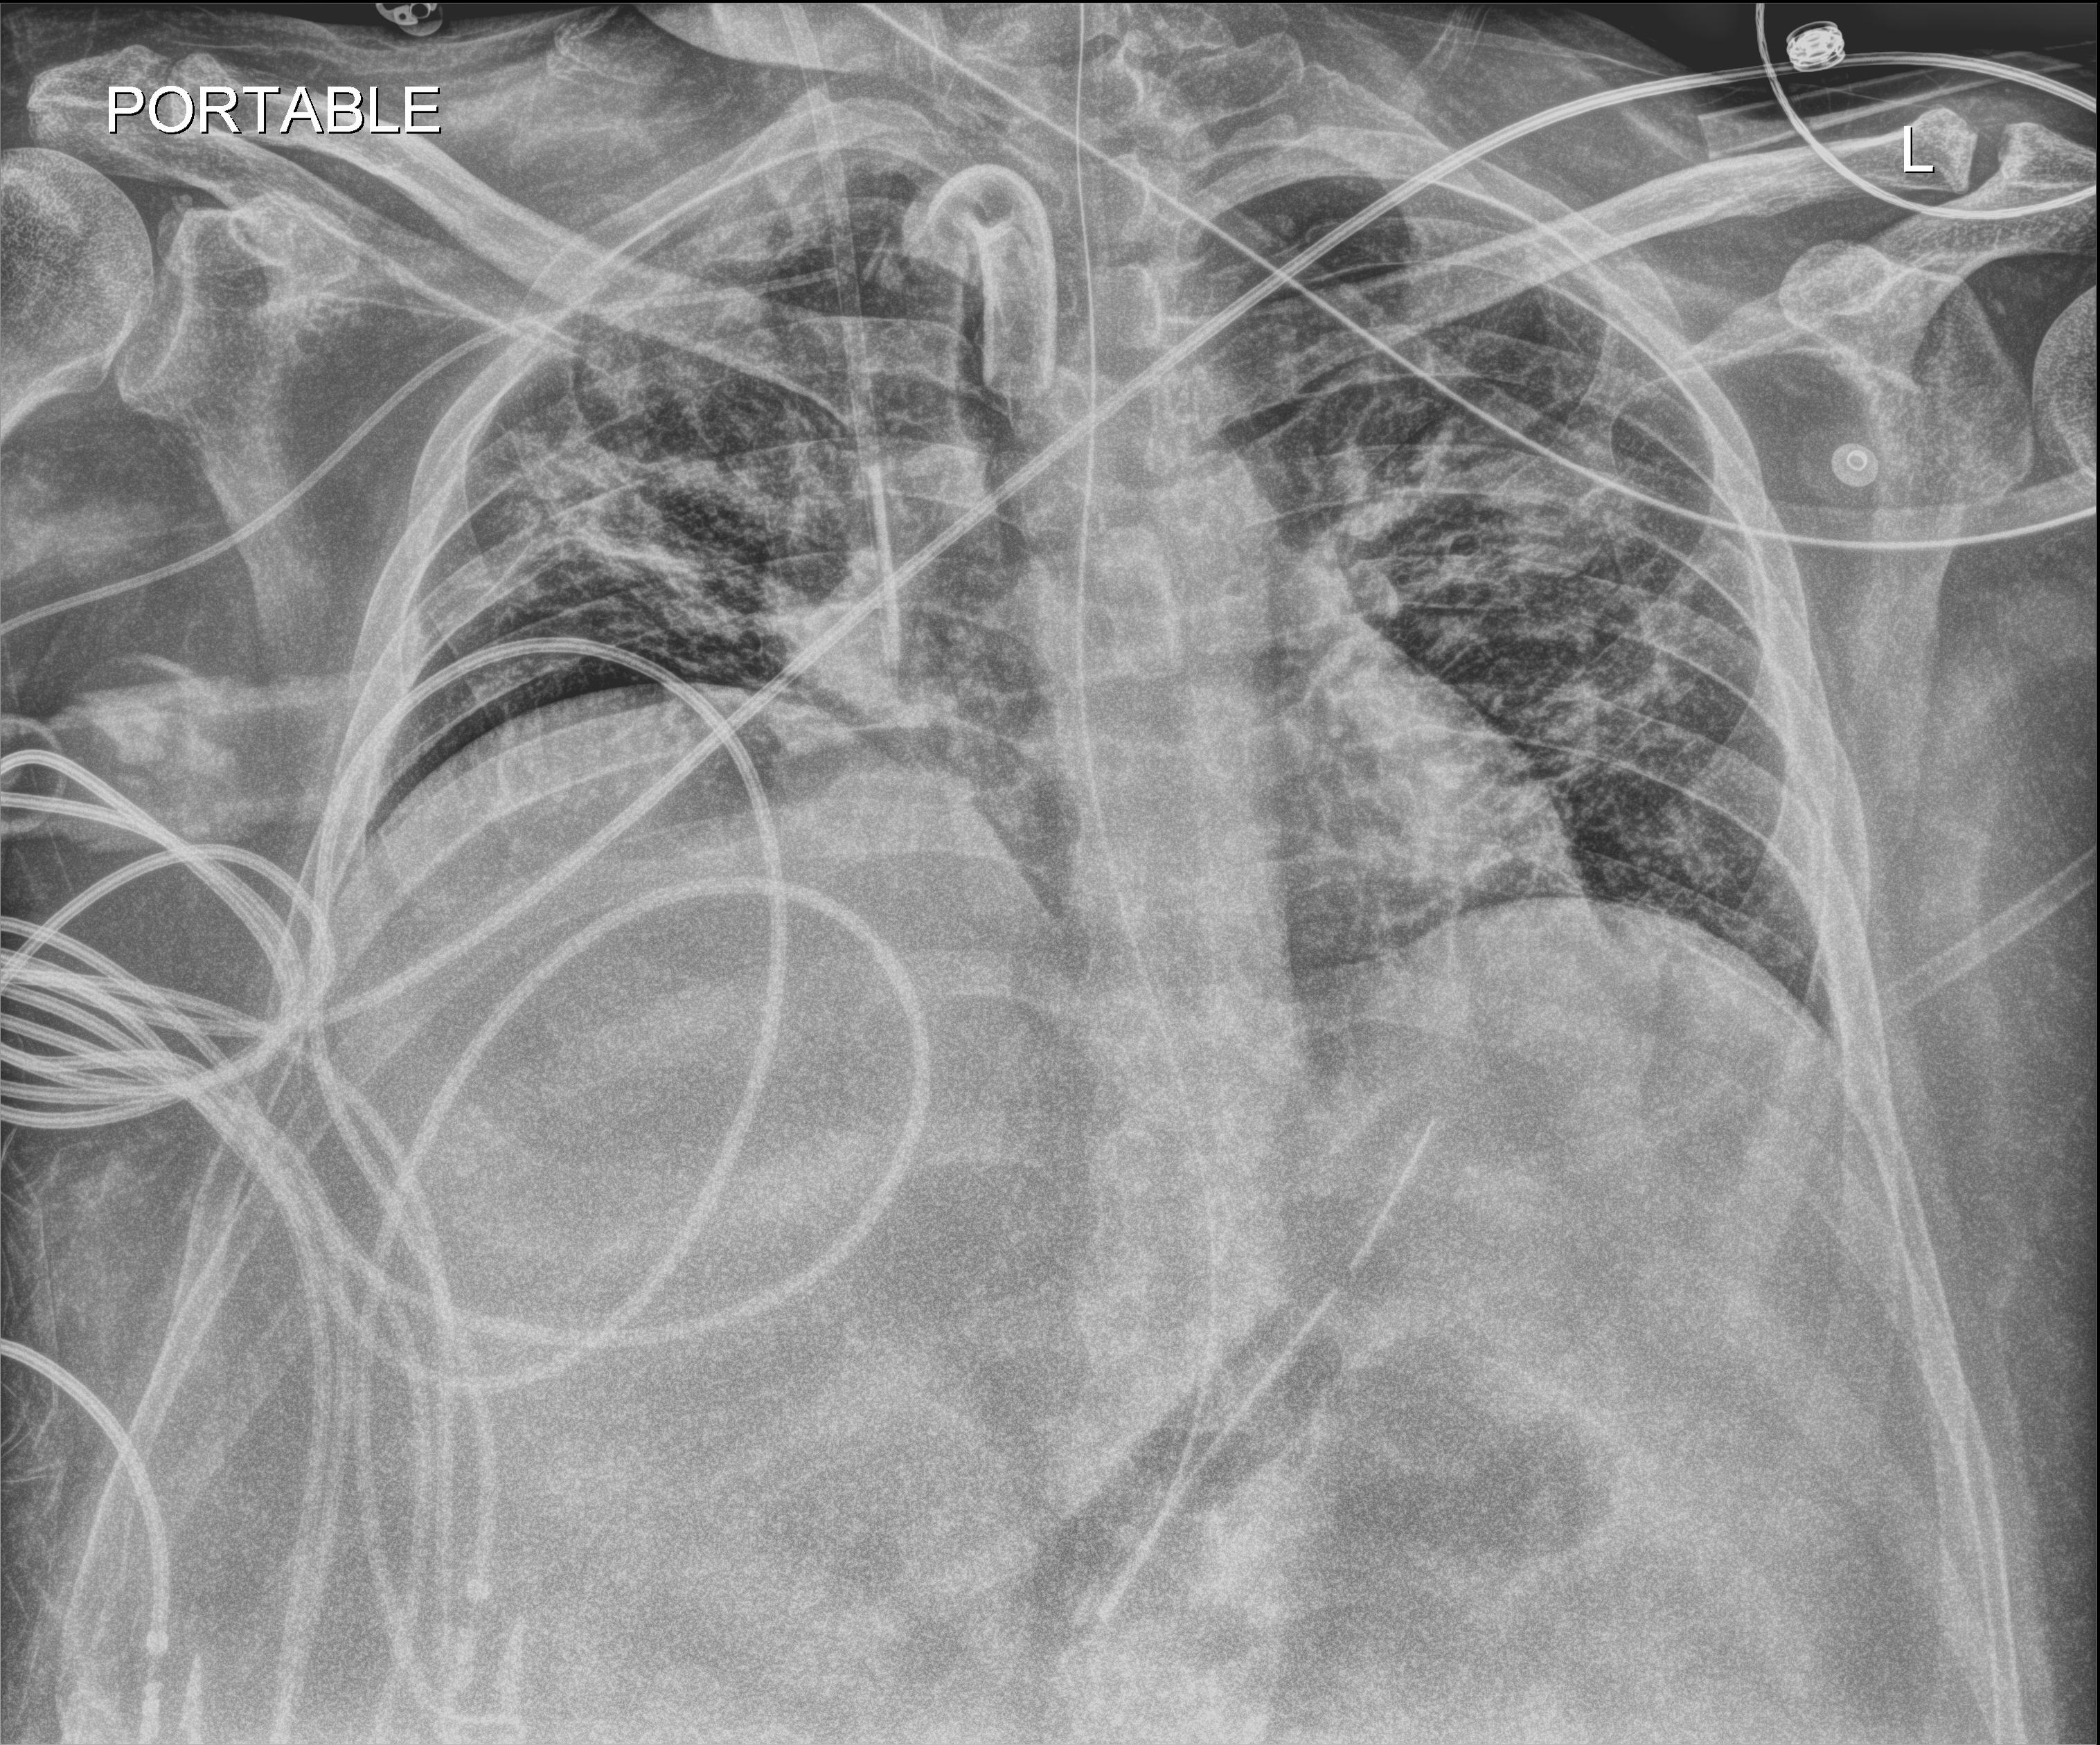
Portable chest radiograph, anteroposterior (AP) projection. Patient hospitalised with COVID-19, aged 18–59 years.
Hospital-stay facts (about this admission, not read from this image; timing relative to this image not recorded): admitted to intensive care during this hospital stay: yes; COPD (admission record): no.